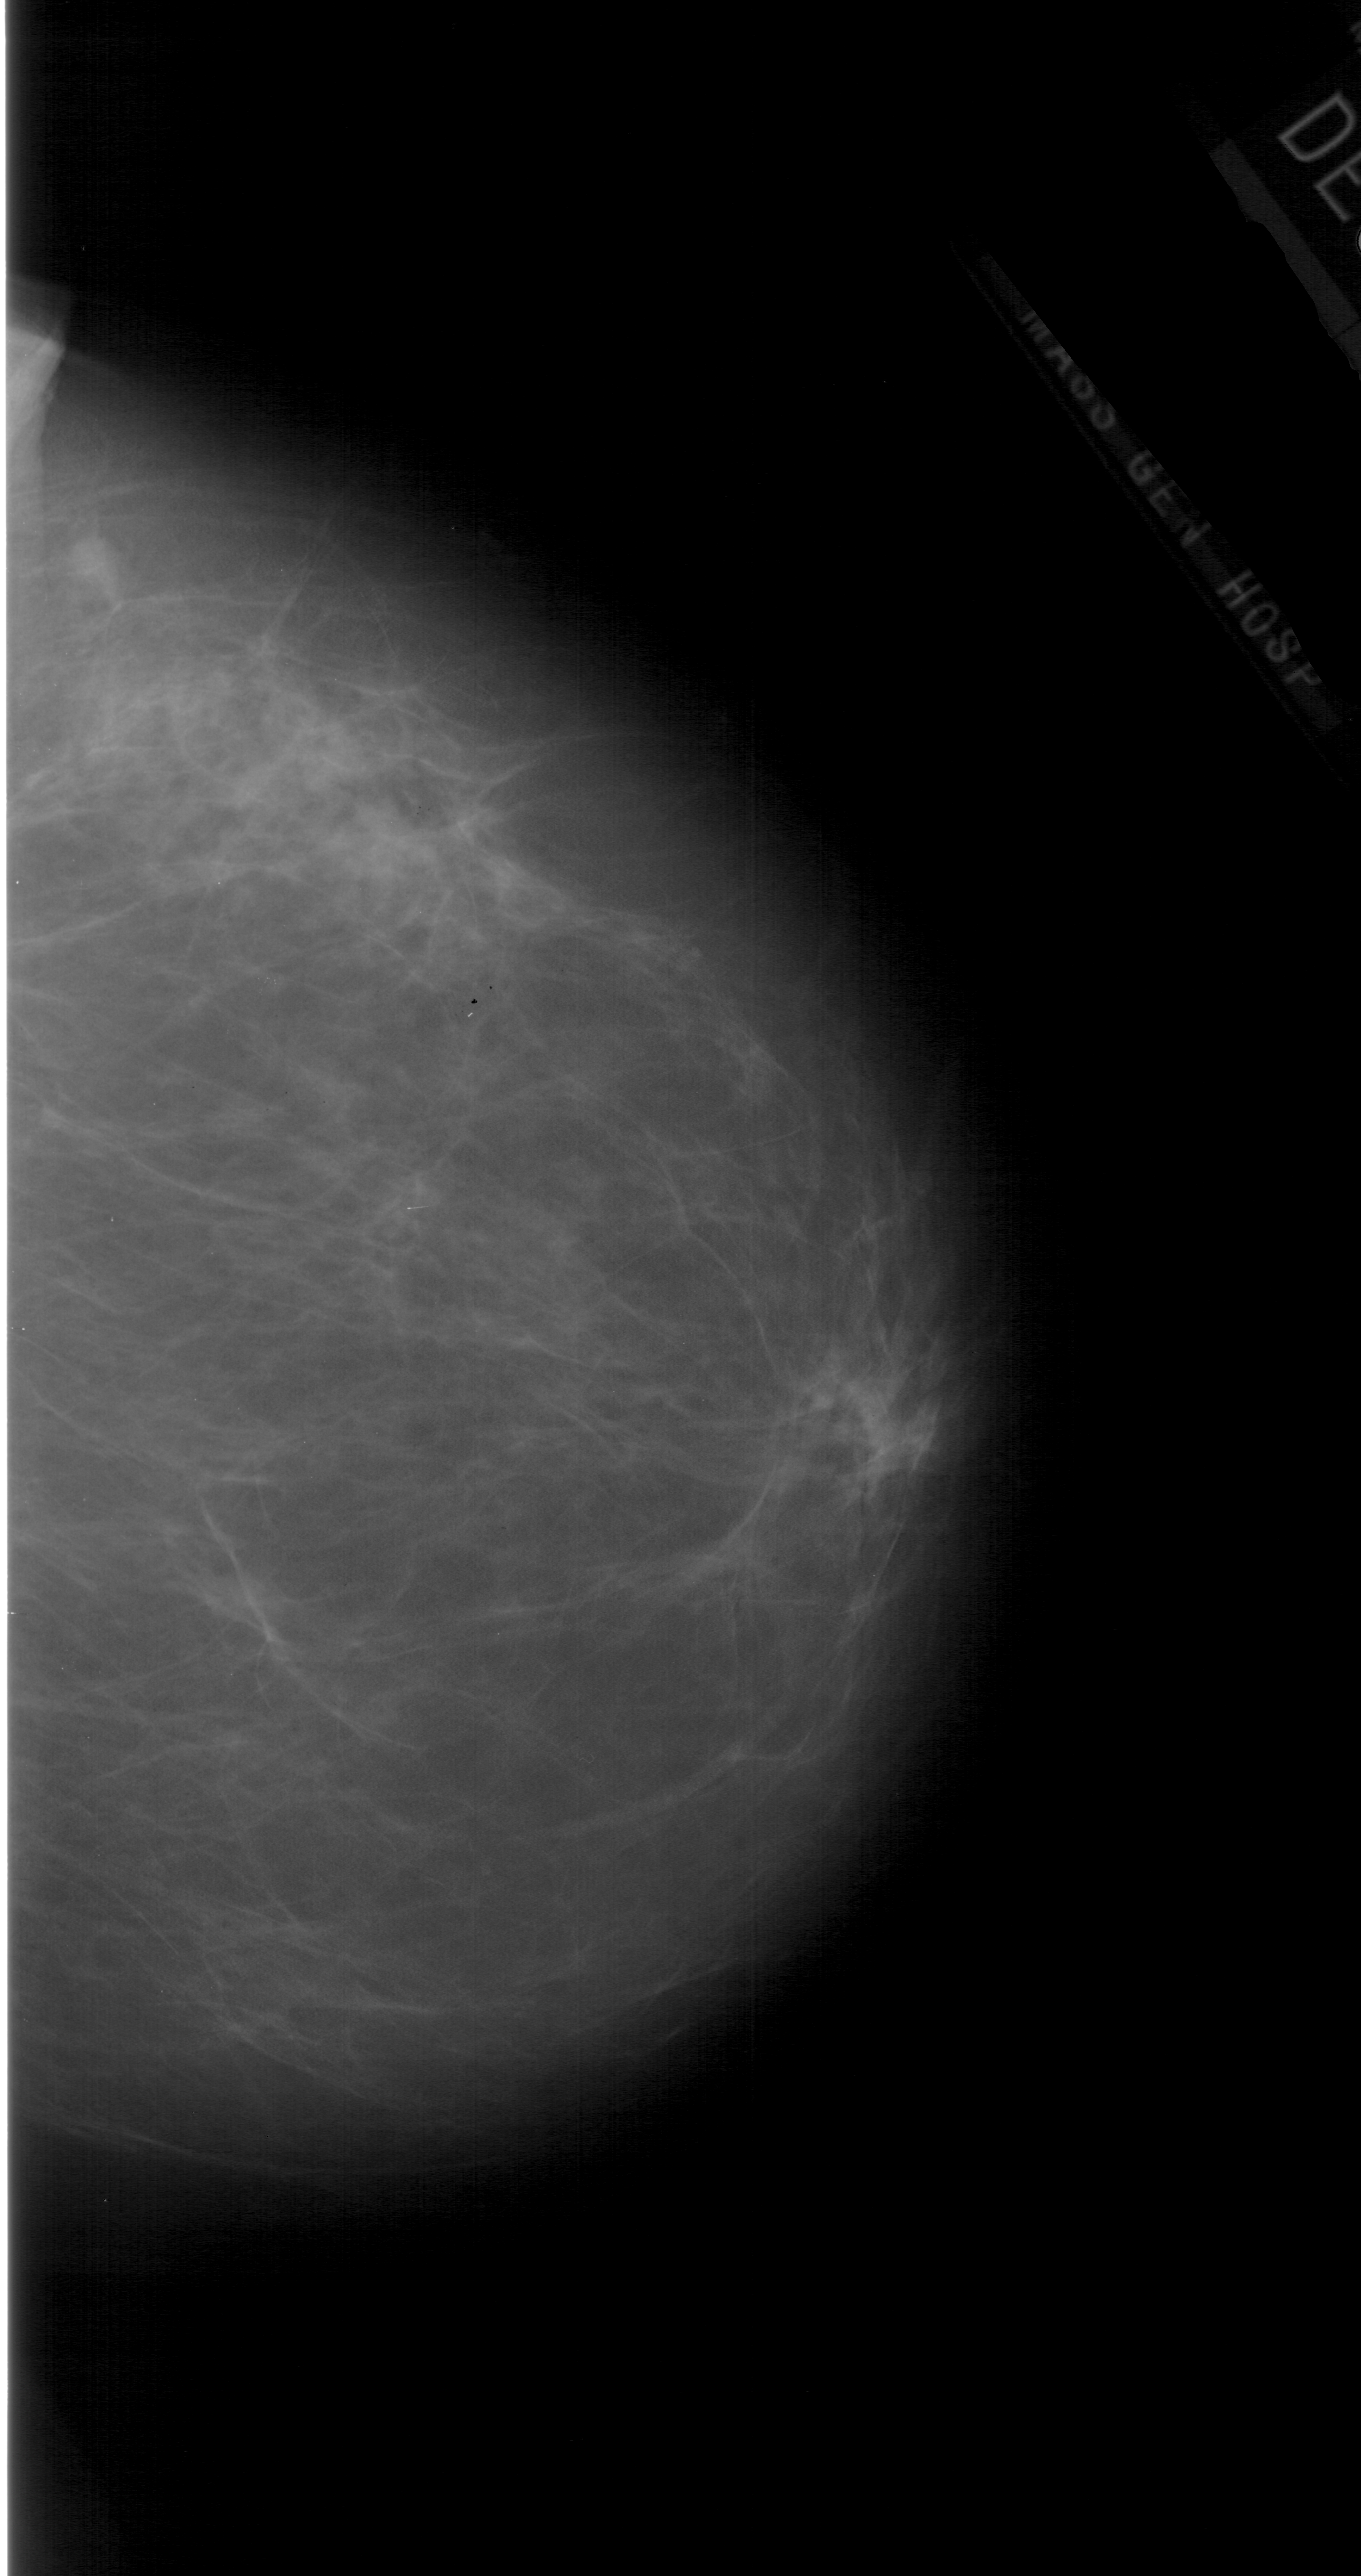
Digitized screen-film mammogram. Right breast. Craniocaudal (CC) view. BI-RADS breast density category 2 (scale 1–4). 1361 × 2576 image matrix.
Marked abnormalities (boxes around the expert regions of interest):
- mass, shape irregular, margins ill defined; BI-RADS assessment category 4; subtlety rating 4 on a 1 (subtle) to 5 (obvious) scale; pathology (as recorded): malignant: bounding box <385,744,544,892> (left, top, right, bottom; pixels)